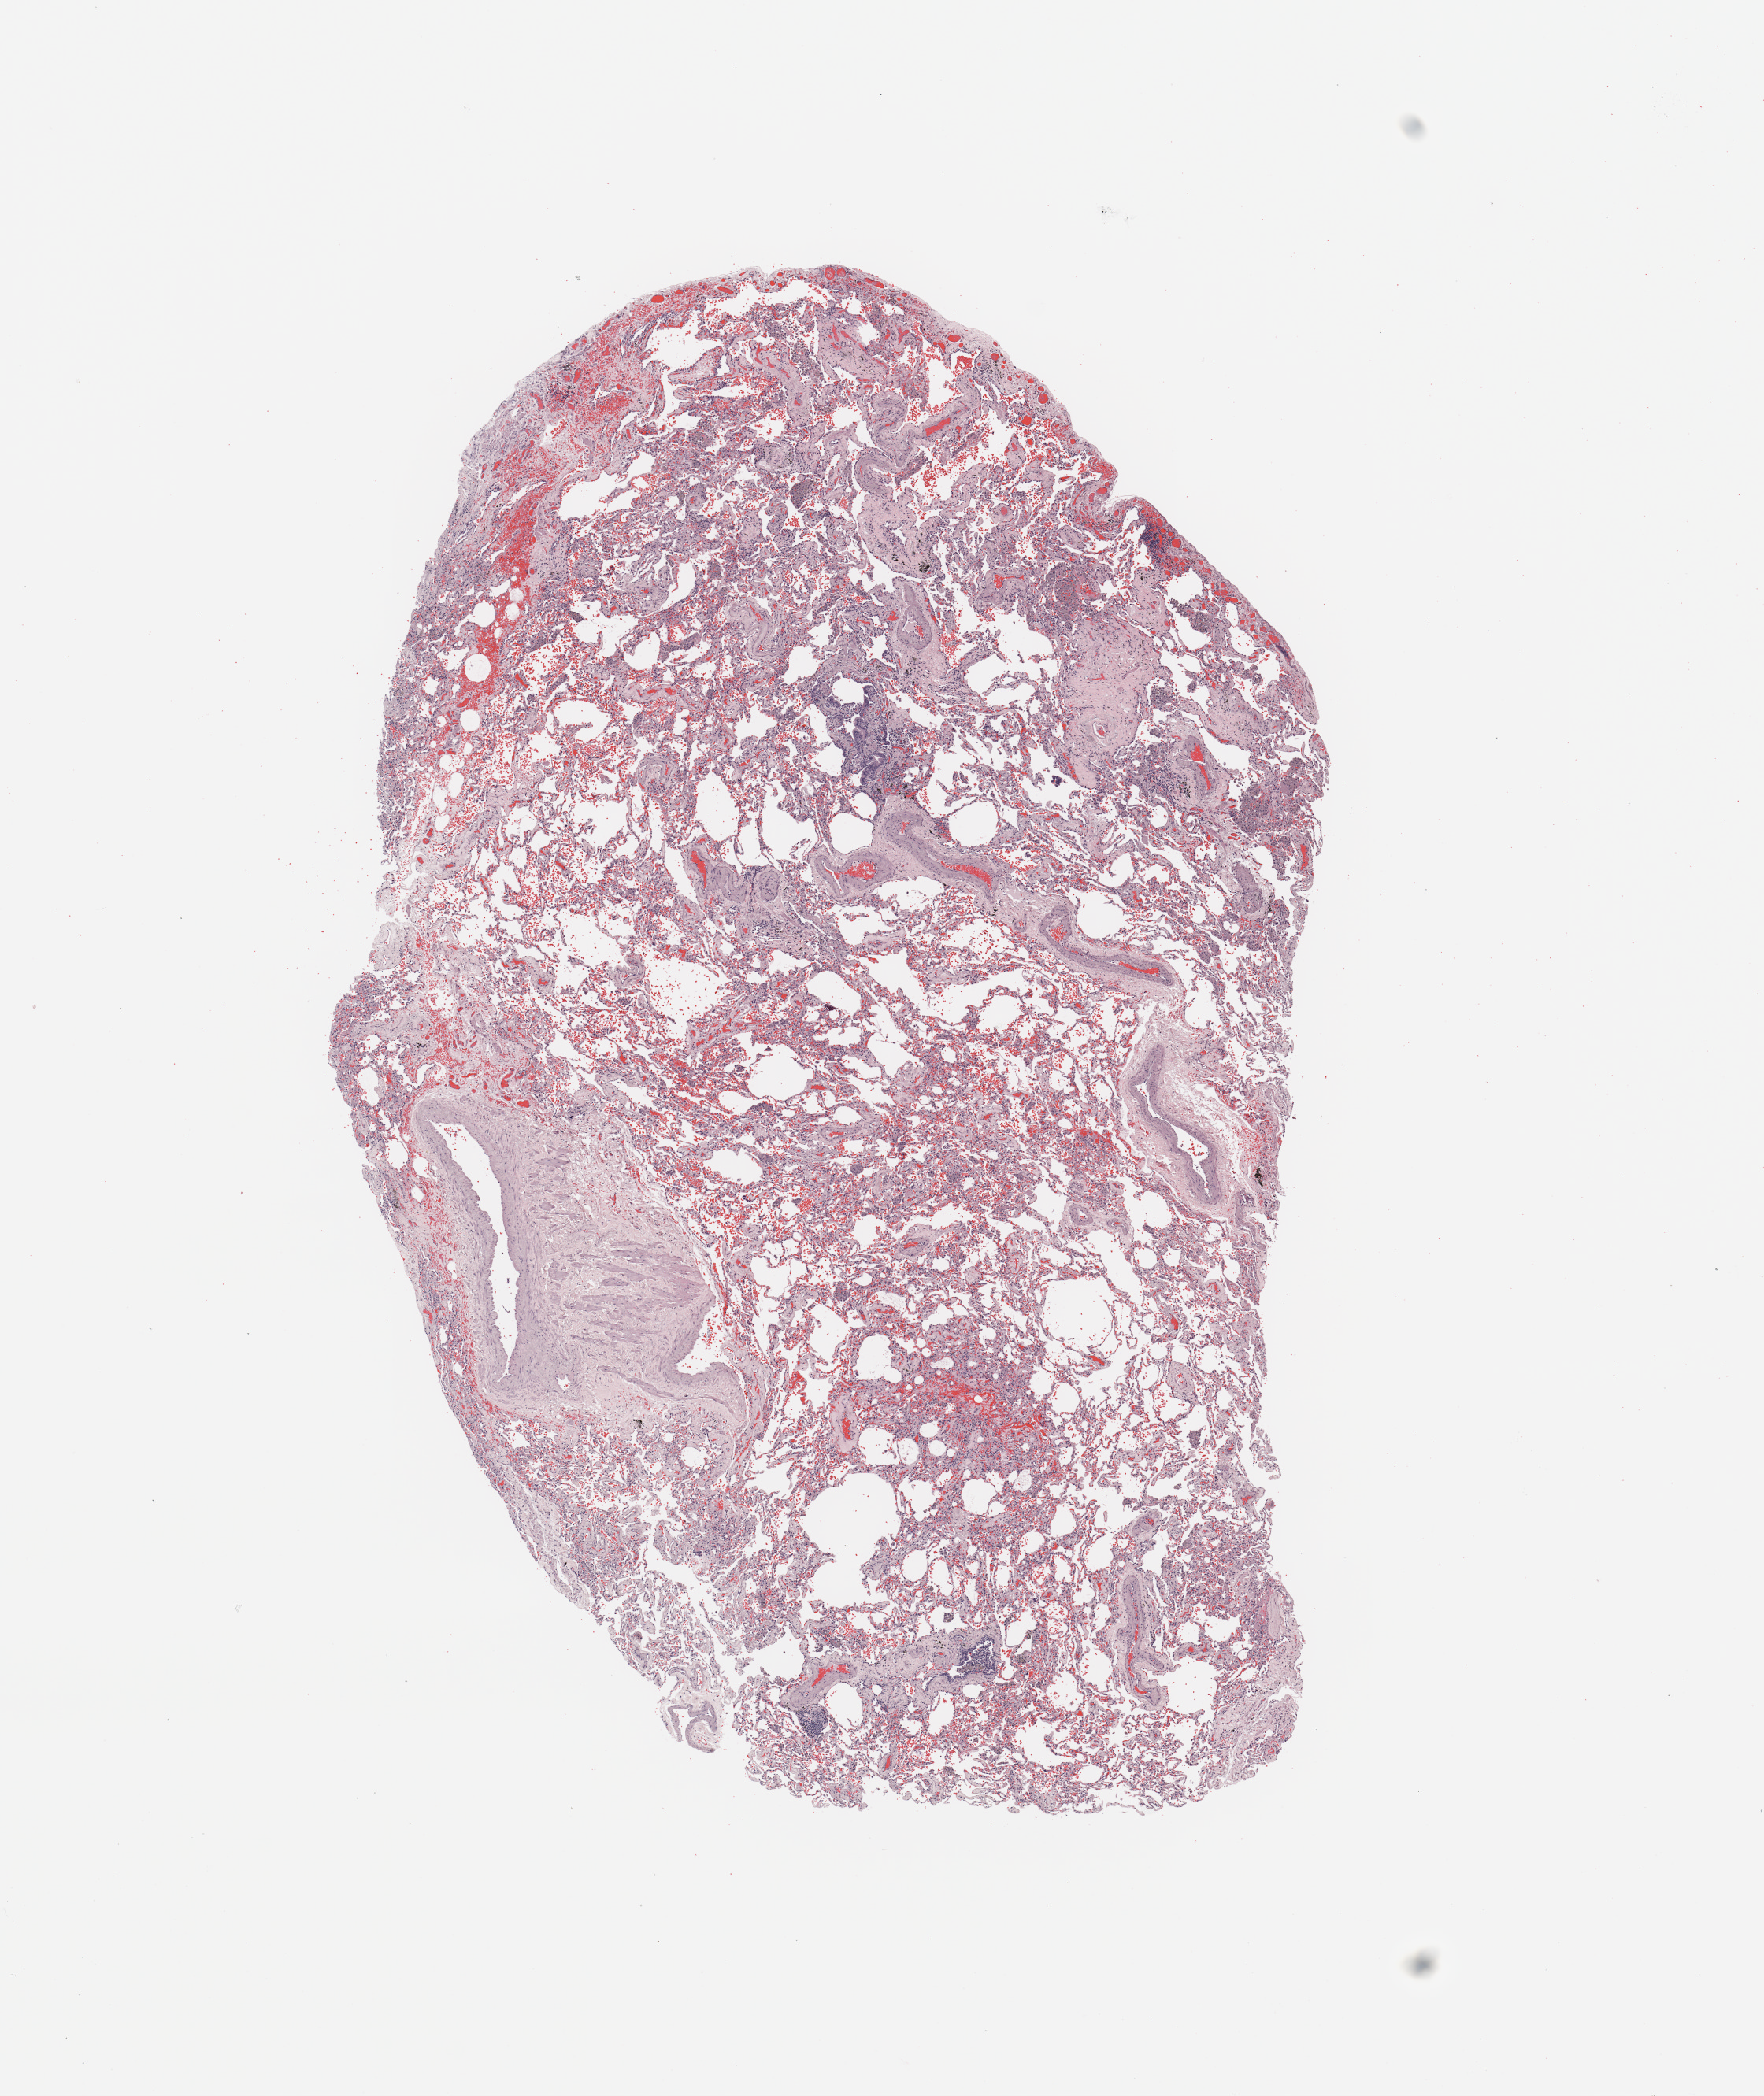
Digitized Hematoxylin and eosin (H&E) stained tissue section (whole slide) — whole scanned area (about 8.9 x 10.5 mm) shown as a low-resolution overview. Normal (non-tumour) tissue sample, sampled site: lung. 66-year-old female patient.
* this section: normal (non-tumour) tissue from the same patient
* patient diagnosis: Adenocarcinoma, NOS